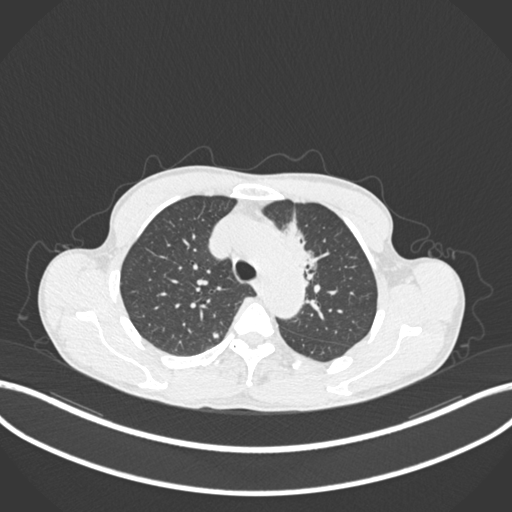
Chest CT, one axial slice; slice 150 of 211 in the series (ordered by position); 120 kVp; lung window (W 1500 / L -600 HU); 1 mm slice thickness; 512 × 512 image matrix, field of view 400 × 400 mm. Patient: male, 58 years. From the clinical record (not read from this slice): clinical TNM (as recorded): T1c N1 M0.
Annotated regions visible in this slice (bounding box drawn by a radiologist):
- lung tumour (recorded histology: adenocarcinoma): bounding box (x1, y1, x2, y2) in pixels: (280, 215, 325, 283)